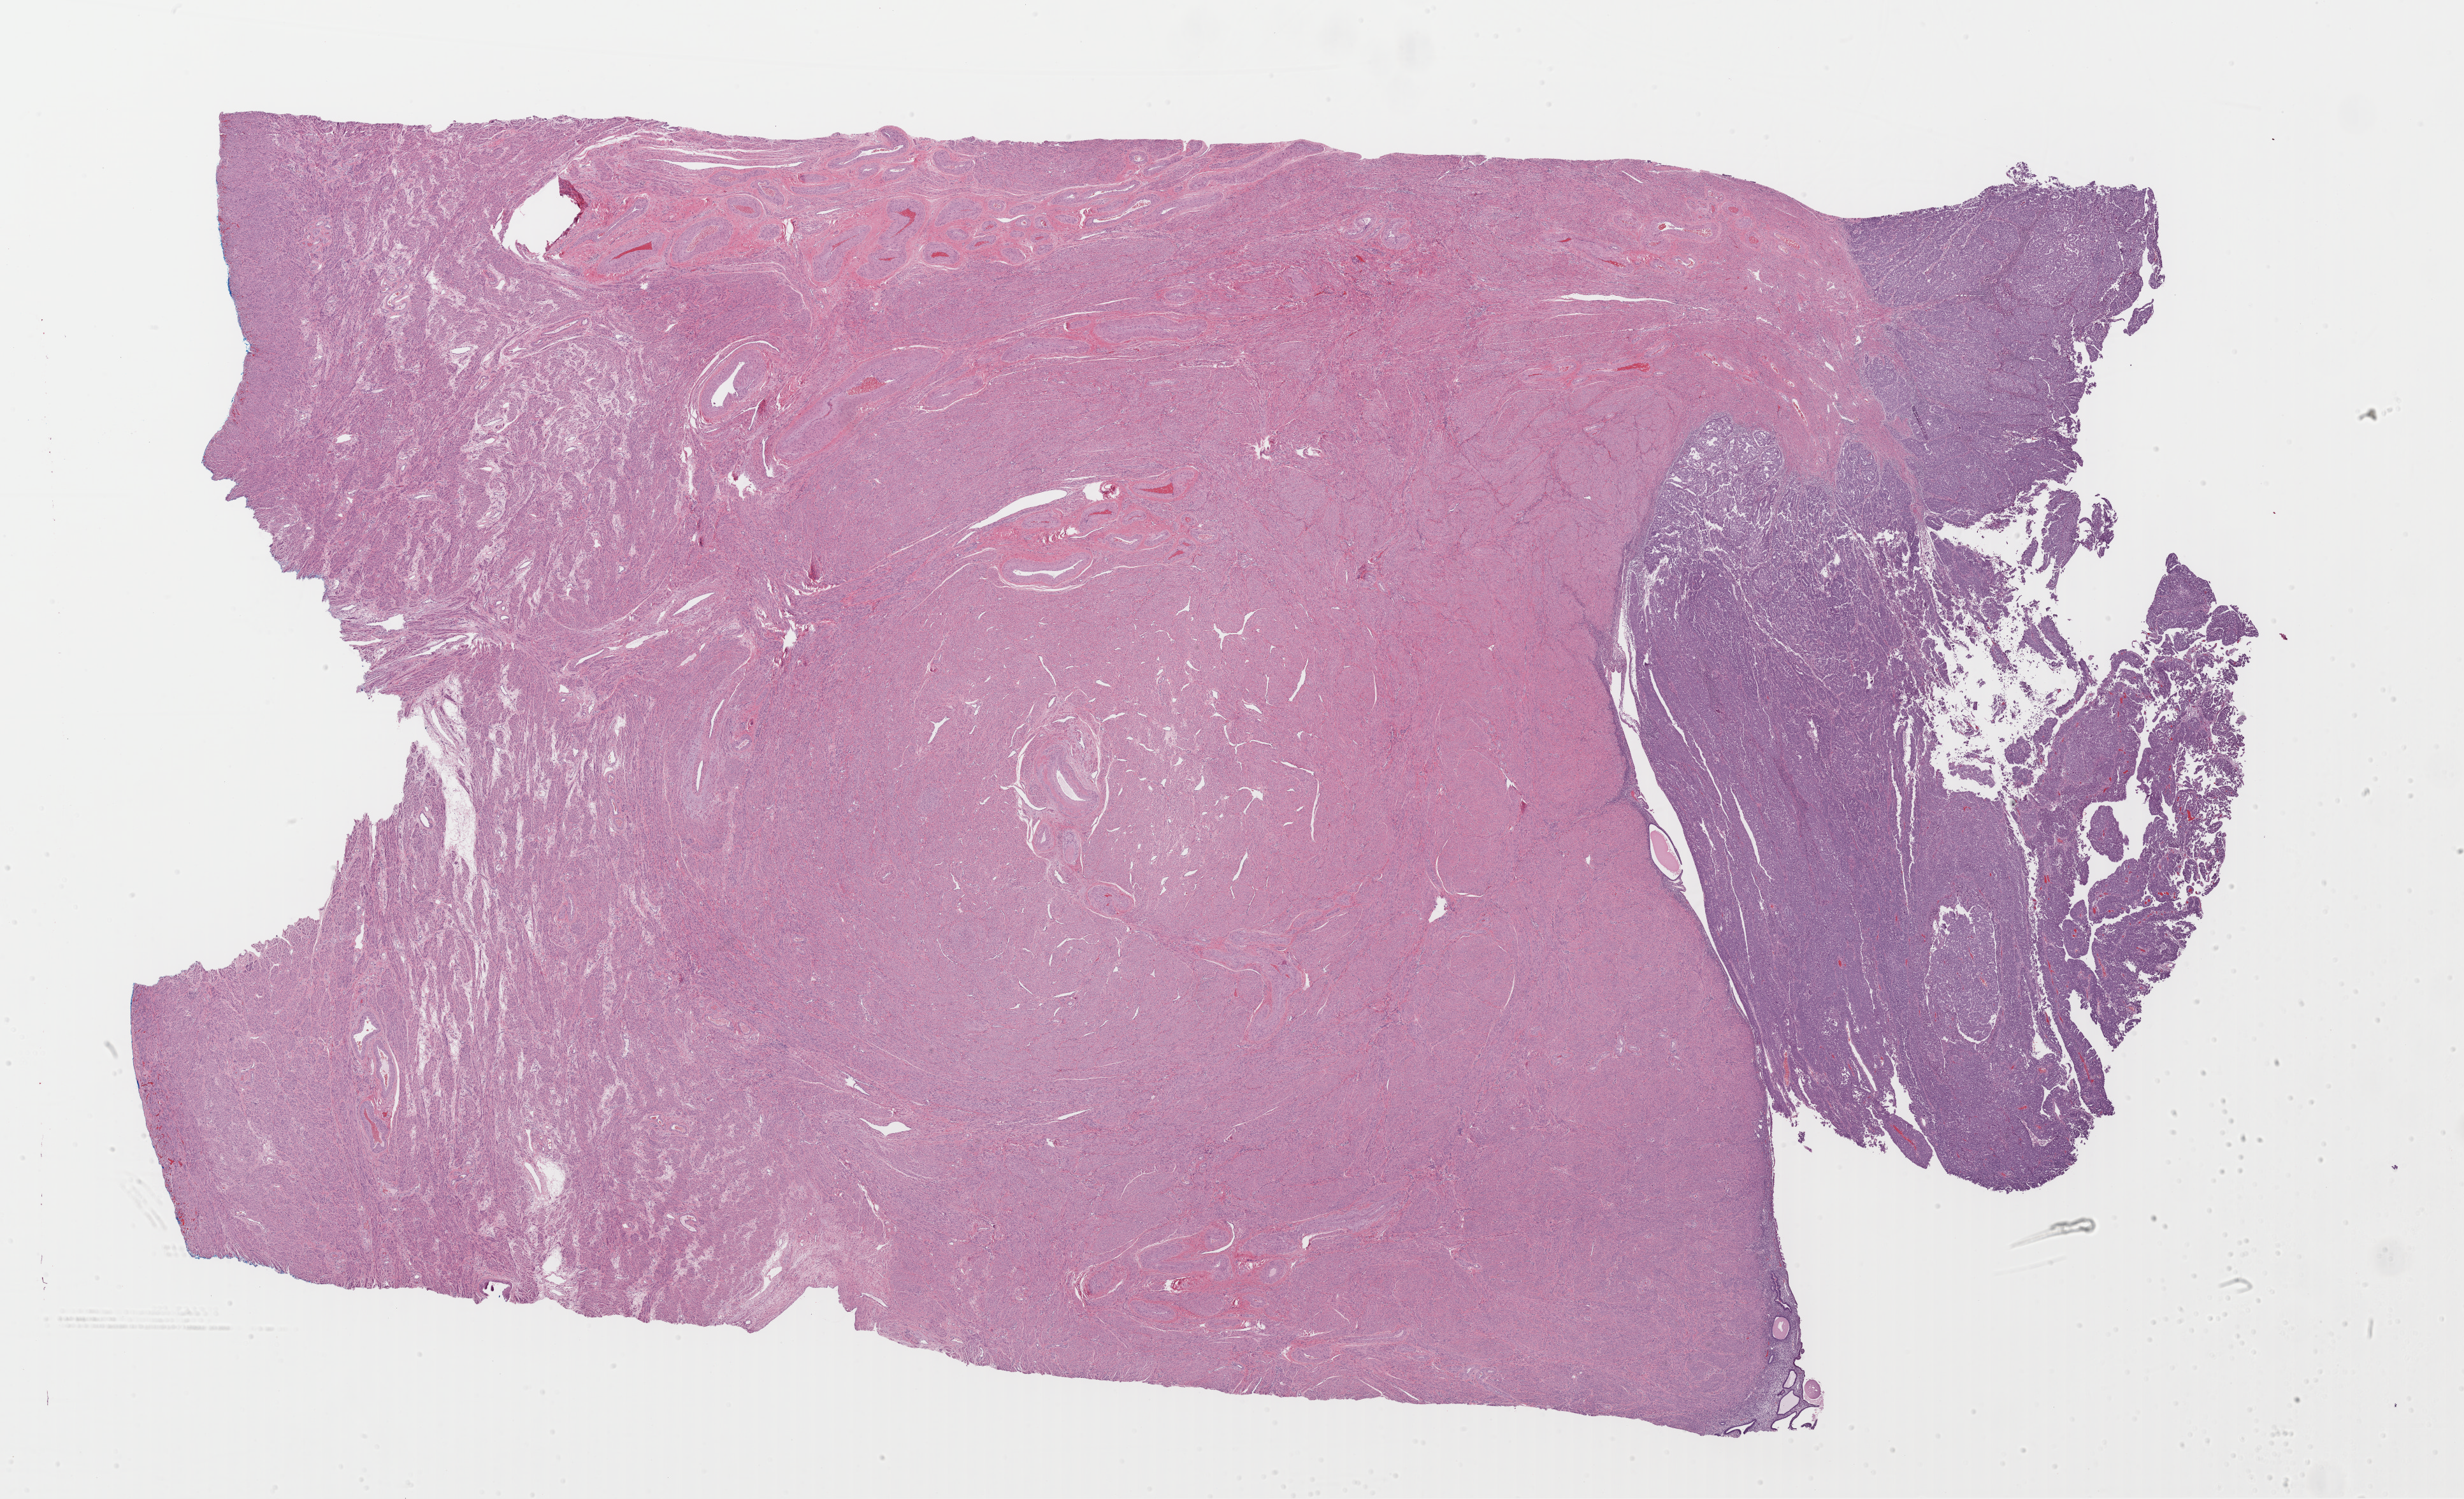
H&E-stained whole-slide image — a low-resolution overview of the entire scanned area, about 30.5 x 18.6 mm. Formalin-fixed paraffin-embedded (FFPE) diagnostic section. Primary tumour sample from the uterus. Female patient; age at initial diagnosis 55 years. Histologic grade: G1 (well differentiated).
Diagnosis: Serous cystadenocarcinoma, NOS (endometrium). FIGO stage: IA.